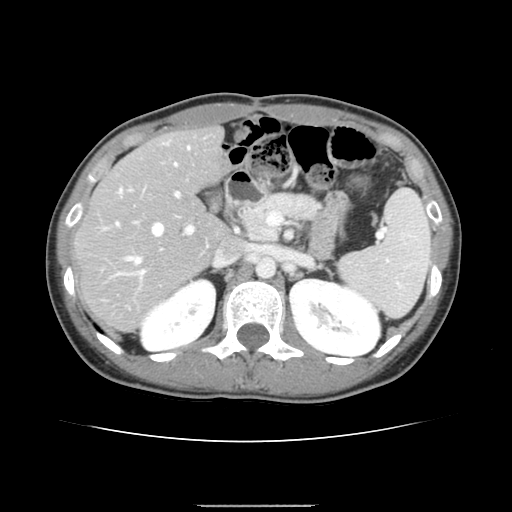
Contrast-enhanced abdominal CT, one axial slice. Position 88 of 150 along the scan axis. 120 kVp. Intravenous contrast given. Soft-tissue window (W 400 / L 40 HU). 2.5 mm slice thickness. 512 × 512 image matrix. Female patient, age 32 years. Case-level facts recorded for this patient, not image findings: diagnosis: colorectal cancer liver metastases, imaged before liver resection; multiple liver metastases: yes; largest metastasis: 0.7 cm; disease in both lobes: no.
Outlined on this slice (outlined manually by an expert reader):
- hepatic veins: bounding box (x1, y1, x2, y2) in pixels: (116, 147, 190, 263)
- liver: (77, 129, 227, 331)
- planned liver remnant (the part of the liver to remain after resection): (77, 128, 226, 277)
- portal vein (with intrahepatic branches): (104, 189, 194, 277)